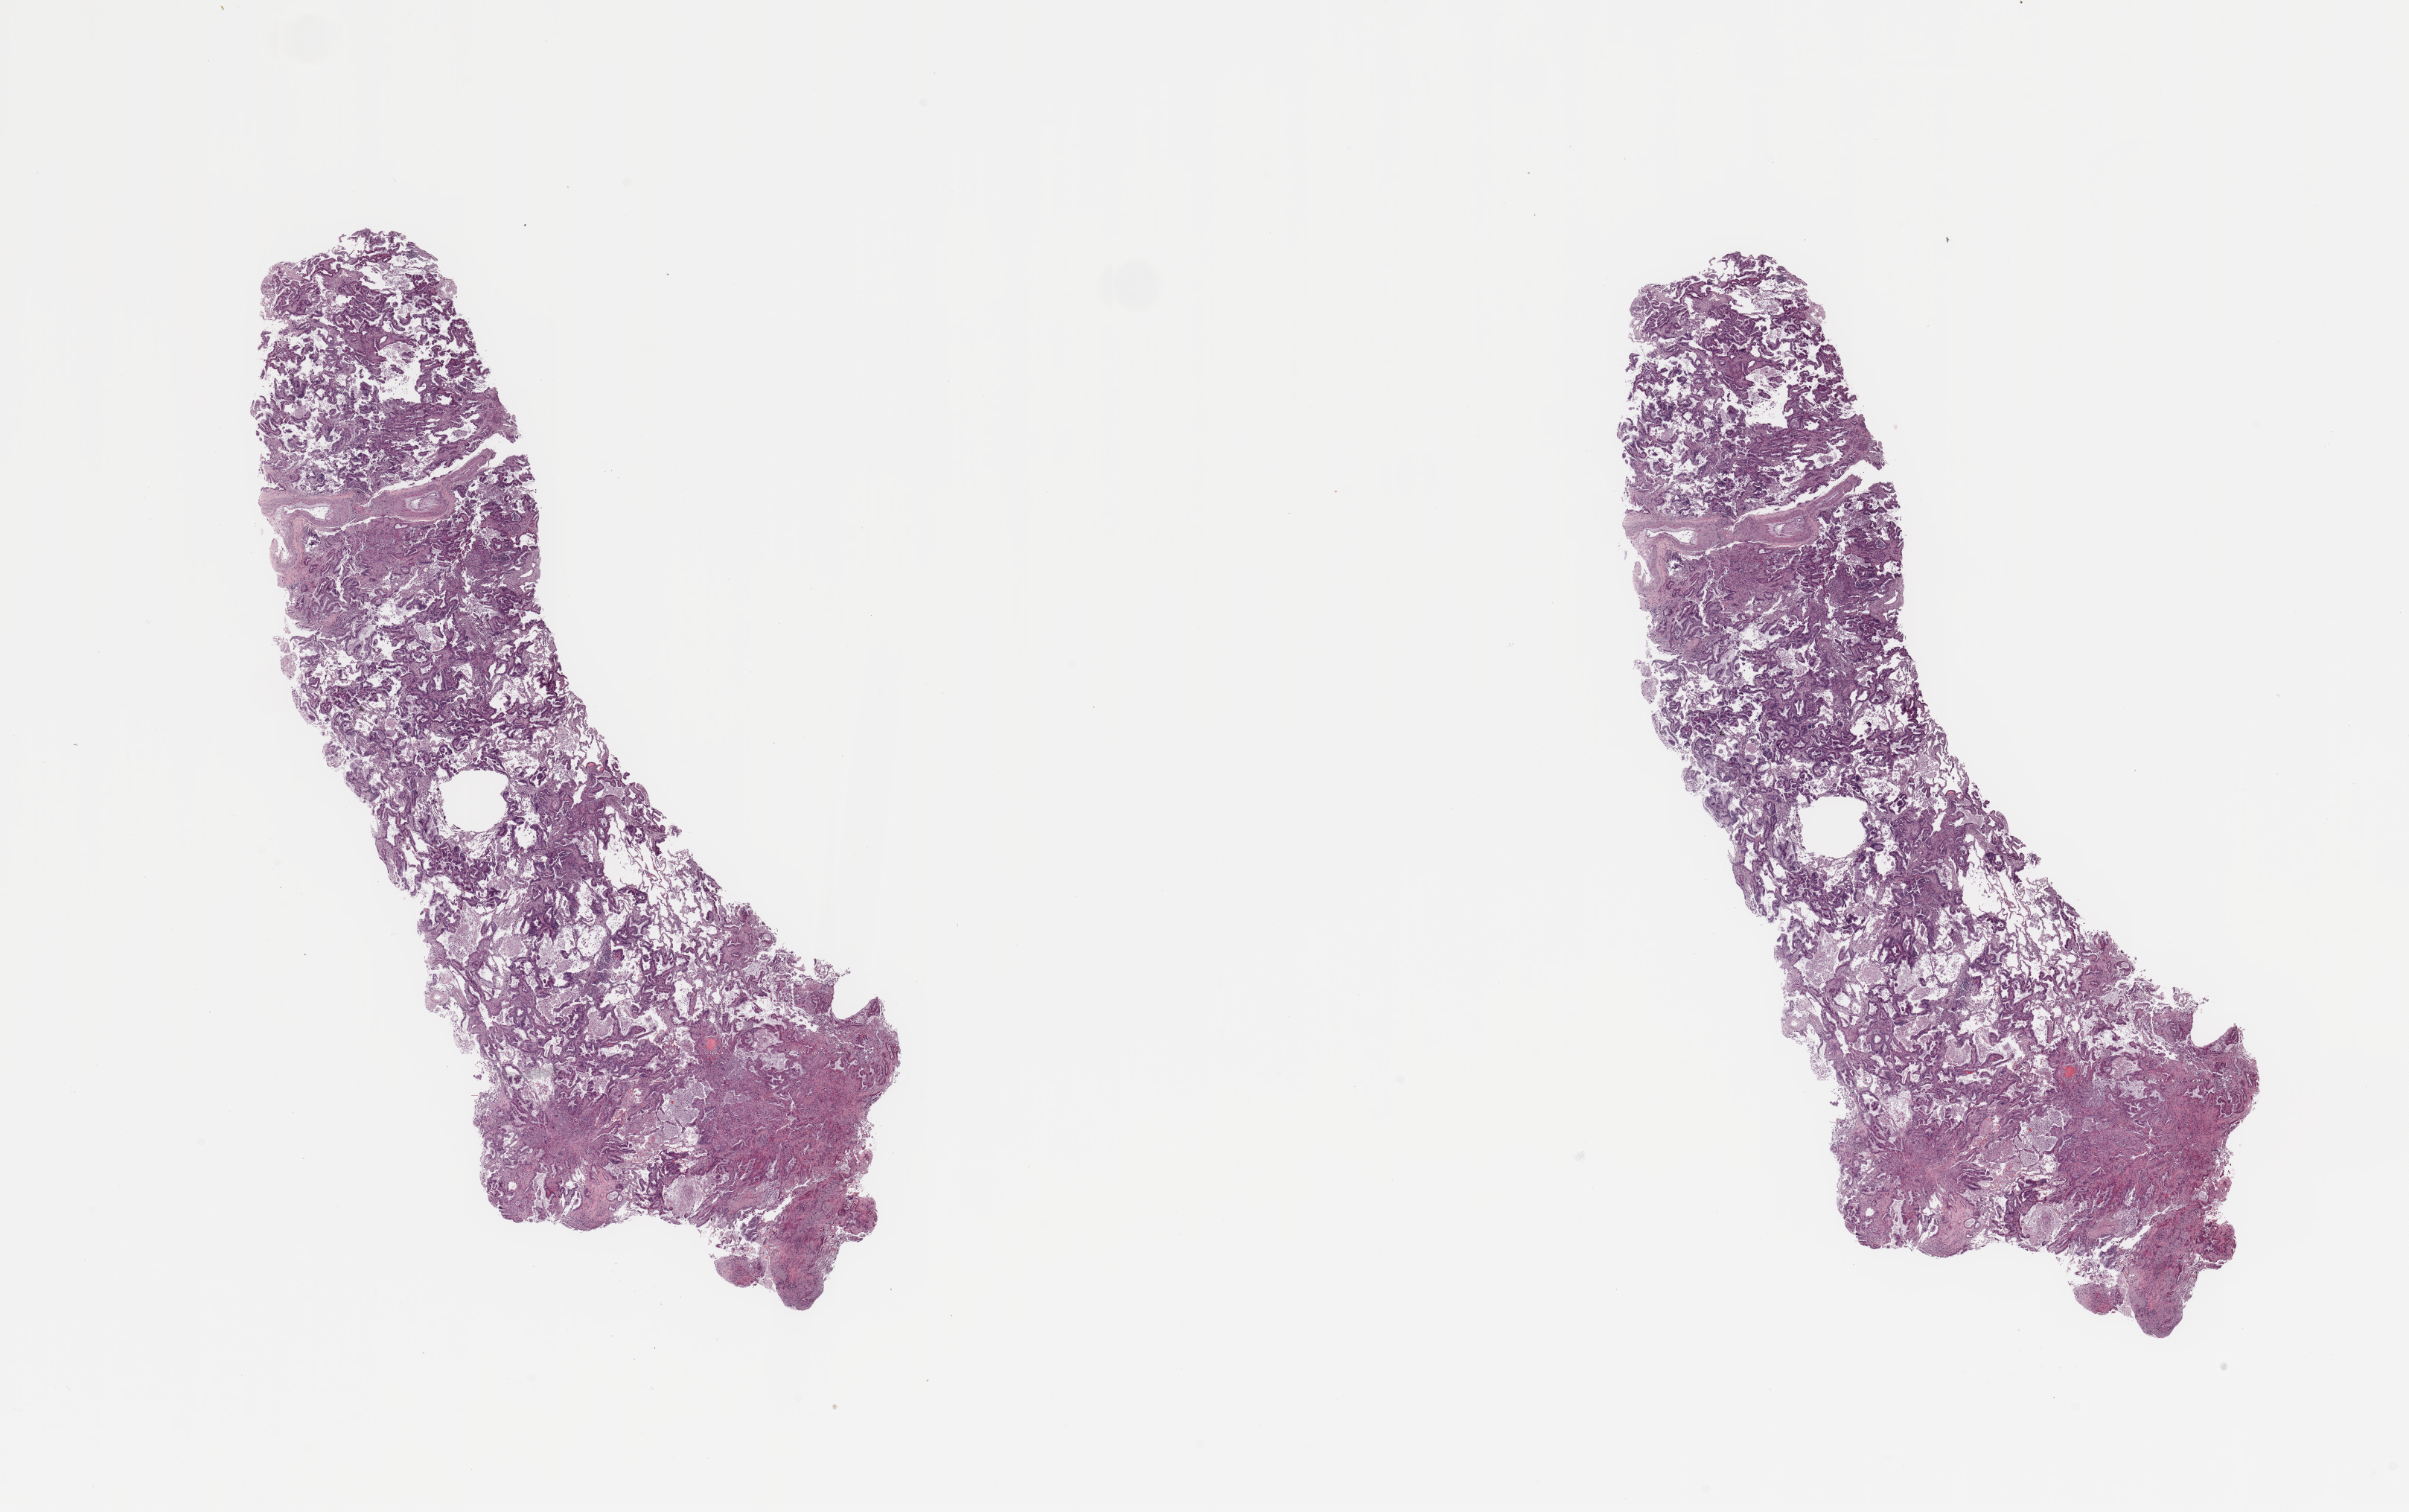
Whole-slide histology image, H&E — low-resolution overview of the scanned area, about 25.6 x 16.1 mm (slide scanned at 20x), tumour tissue sample, sampled site: lung. Female, 79 y/o. Histologic grade: G1 (well differentiated). Slide review estimates, as recorded: tumour nuclei 70%, necrosis 10%.
* diagnosis: Adenocarcinoma, NOS
* AJCC pathologic stage: IIB